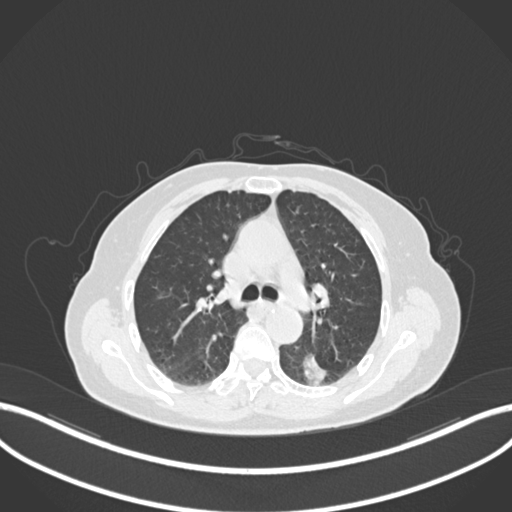
Chest CT, one axial slice. Position 541 of 727 along the scan axis. Reconstruction kernel B30f. 120 kVp. Lung window (W 1500 / L -600 HU). 512 × 512 image matrix, field of view 400 × 400 mm. Female patient, age 70 years. Case-level facts recorded for this patient, not image findings: clinical TNM (as recorded): T1c N0 M0.
Annotated regions visible in this slice (rectangle marked by the reading radiologist):
- lung tumour (recorded histology: adenocarcinoma): bounding box [x1, y1, x2, y2] px = [298, 351, 328, 385]